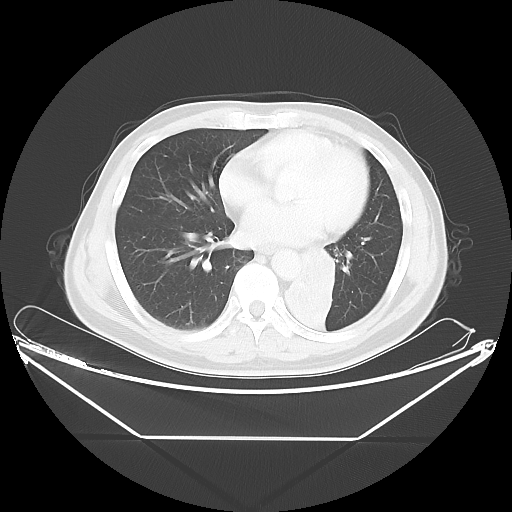
Chest CT, one axial slice. Slice 19 of 48 in the series (ordered by position). 120 kVp. Lung window (W 1500 / L -600 HU). 512 × 512 image matrix, field of view 438 × 438 mm. Male patient, age 58 years. From the clinical record (not read from this slice): clinical TNM (as recorded): T3 N3 M0.
Structures marked on this image (bounding box drawn by a radiologist):
- lung tumour (recorded histology: squamous cell carcinoma): bounding box <270,235,362,363> (left, top, right, bottom; pixels)